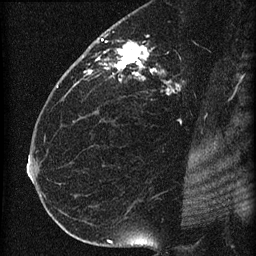
Breast MRI (dynamic contrast-enhanced), one sagittal slice. Dynamic contrast-enhanced series, image 2 of 4 at this slice position (ordered by acquisition). 1.5 T. TE 4.2 ms, TR 22.7 ms. 256 × 256 image matrix, field of view 180 × 180 mm. Patient: female, 35 years. From the clinical record (not read from this slice): setting: breast cancer imaged before/during neoadjuvant chemotherapy; receptor status: HR-positive, HER2-negative.
Structures marked on this image (semi-automatic segmentation, software-assisted and operator-edited):
- analysis volume of interest (the breast-tissue region the enhancement analysis was run in; not a lesion): bounding box <69,27,199,112> (left, top, right, bottom; pixels)
- tumour enhancement mask (voxels above the 90 % enhancement threshold inside the analysis volume of interest): <76,38,171,93>